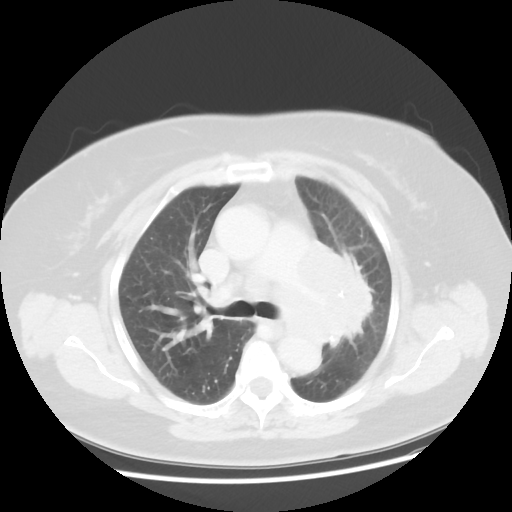
Chest CT, one axial slice; slice 30 of 49 in the series (ordered by position); 120 kVp; lung window (W 1500 / L -600 HU); 512 × 512 image matrix, field of view 374 × 374 mm. Female patient, age 58 years. From the clinical record (not read from this slice): clinical TNM (as recorded): T4 N3 M0.
Outlined on this slice (rectangle marked by the reading radiologist):
- lung tumour (recorded histology: small cell carcinoma): bounding box [x1, y1, x2, y2] px = [284, 241, 369, 345]